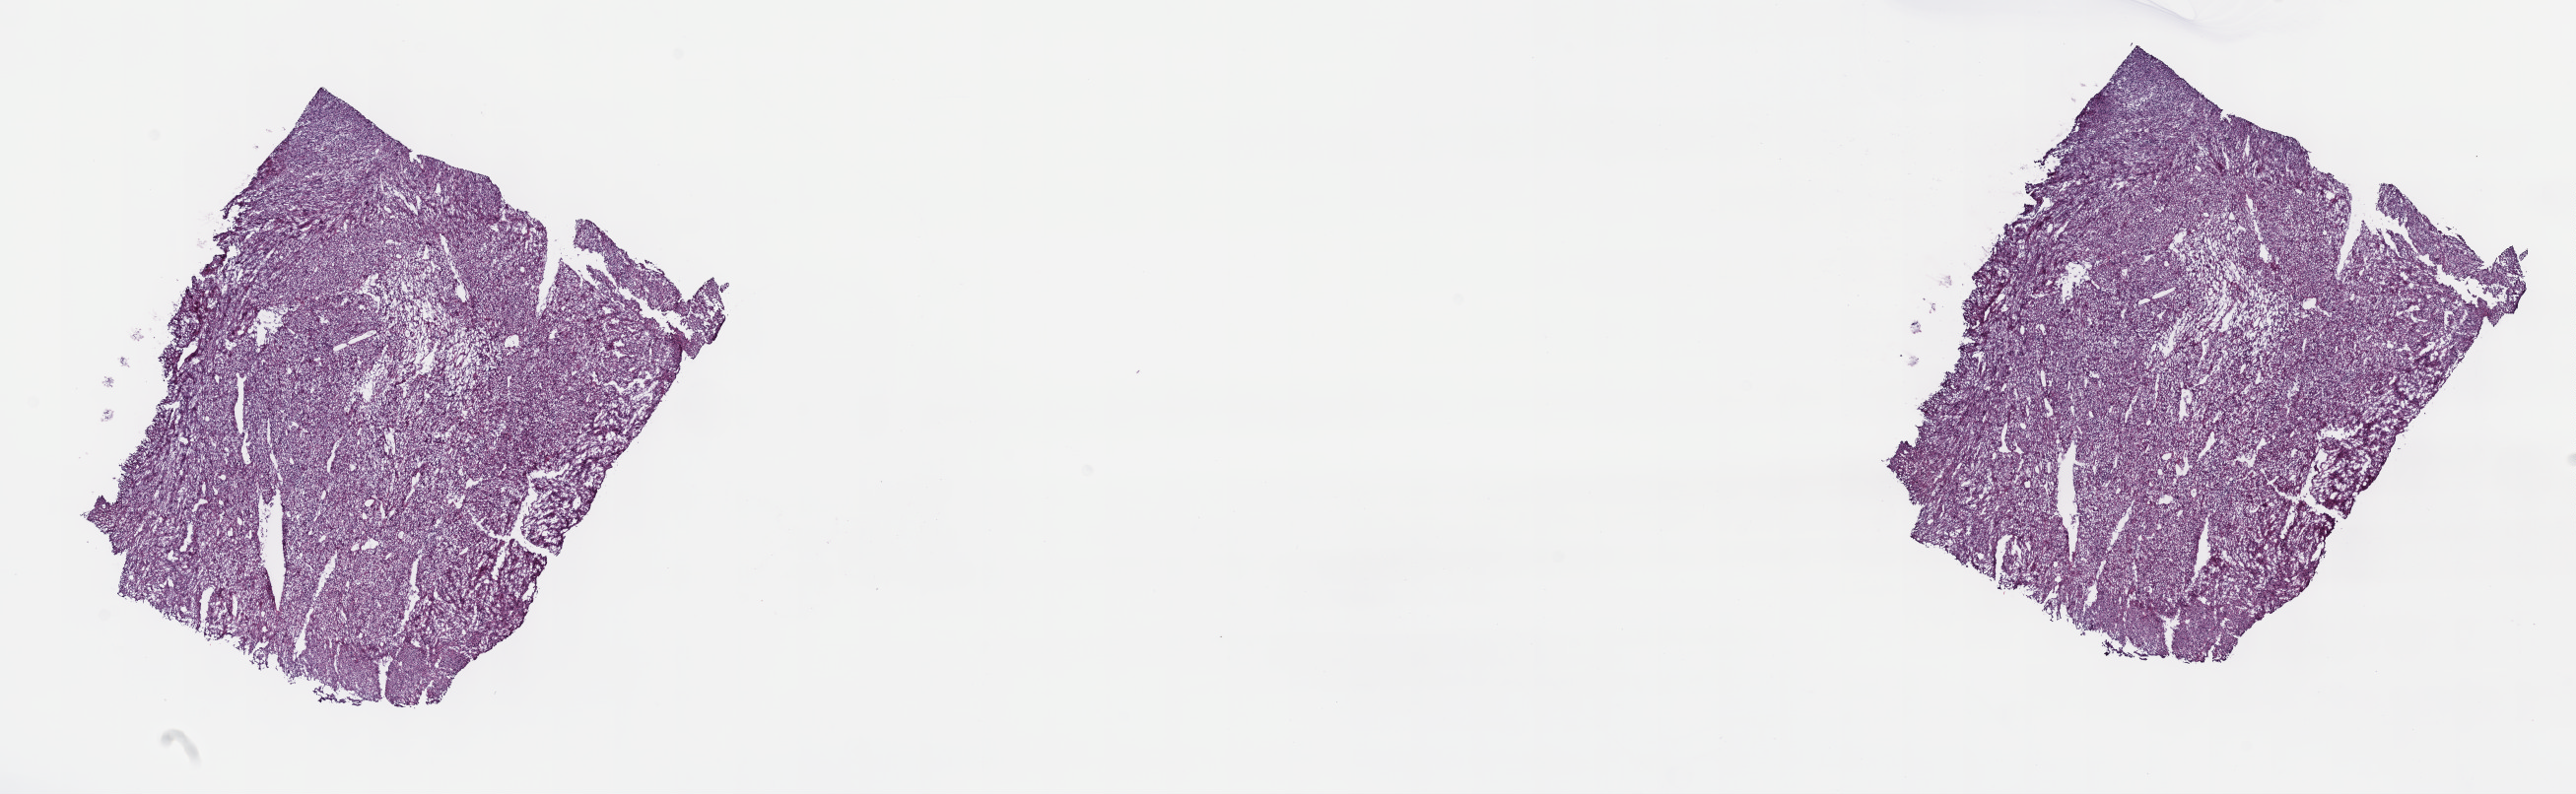
Whole-slide histology image, H&E — low-resolution overview of the scanned area, about 21.1 x 6.5 mm. Frozen section from the top of the tissue portion. Primary tumour sample from the retroperitoneum and peritoneum. Female, age 53 years at initial diagnosis. Composition of this section per pathologist review: tumour cells 100%, tumour nuclei 80%, normal cells 0%, stromal cells 0%, necrosis 0%. Infiltration values recorded for this section: lymphocyte infiltration 1%, monocyte infiltration 0%, neutrophil infiltration 0%.
- diagnosis: Leiomyosarcoma, NOS (retroperitoneum)